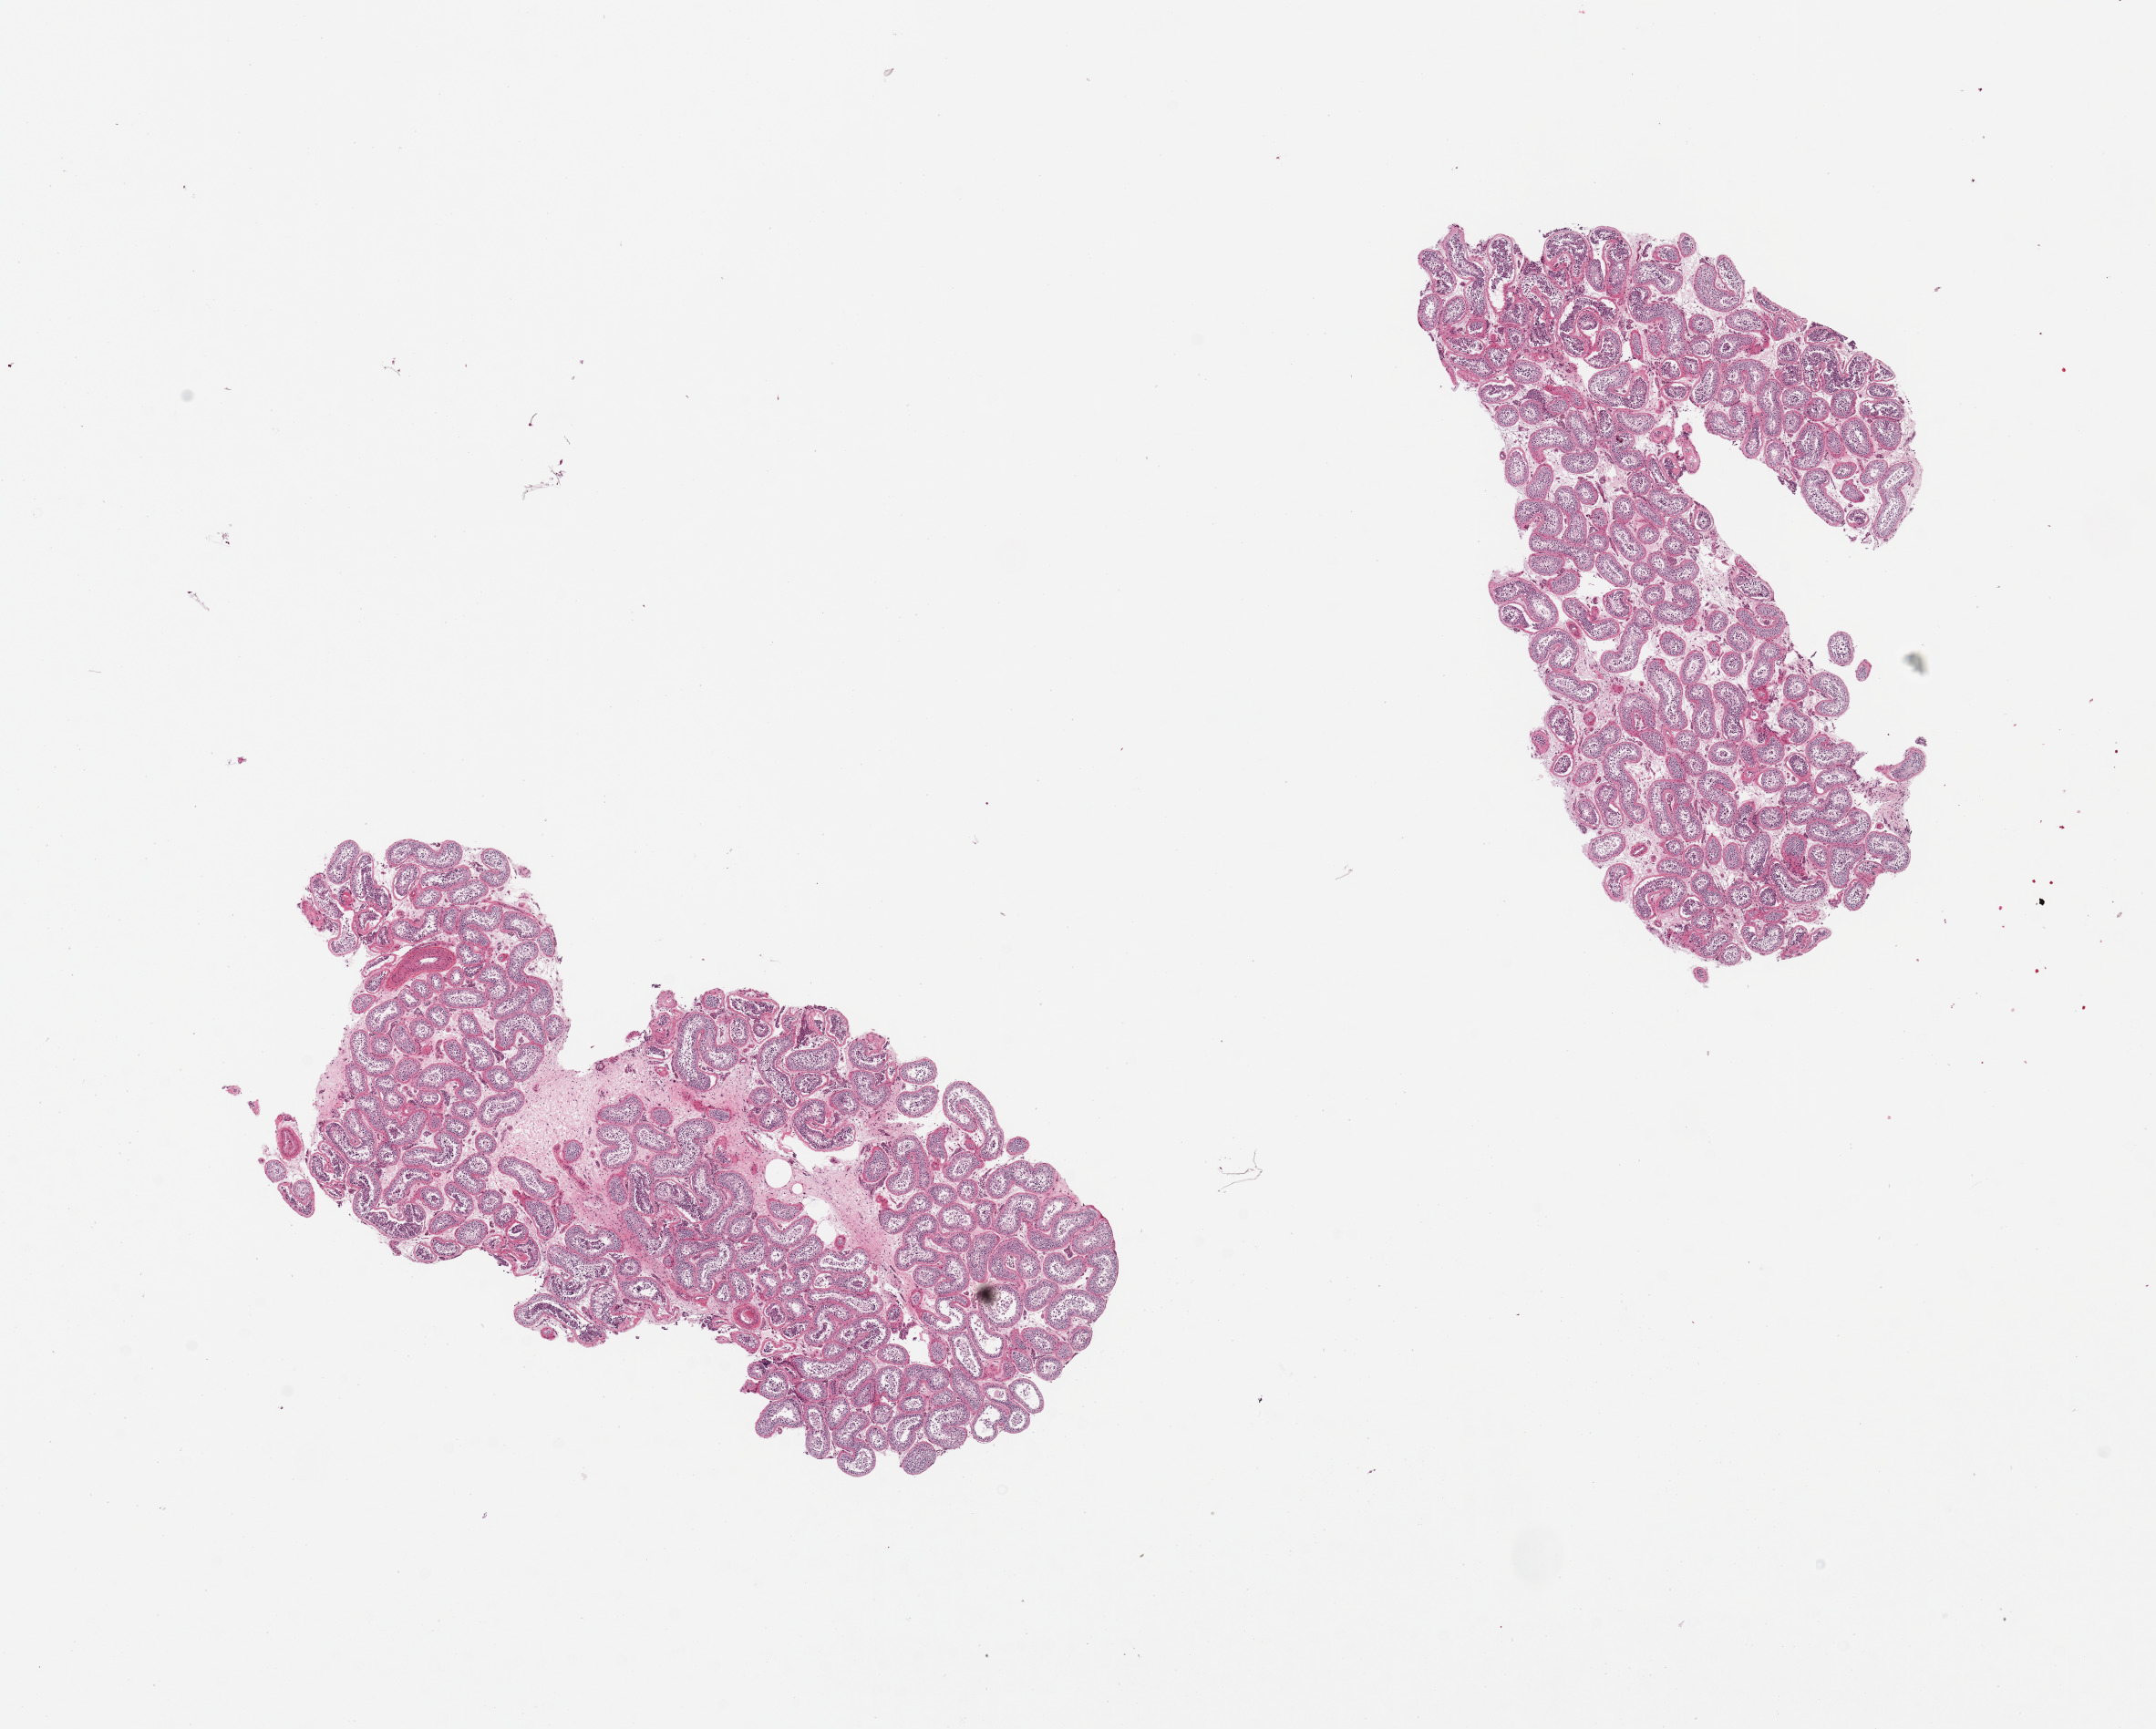
Whole-slide image, haematoxylin and eosin stain — shown as a low-resolution overview of the whole scanned area (about 18.7 x 15.0 mm, acquisition: 20x scan), PAXgene-fixed, paraffin-embedded tissue, section of testis (target tissue), tissue donor sample. Donor: male.
Pathologist's review note for this sample: 2 pieces; spermatogenesis is present but reduced.